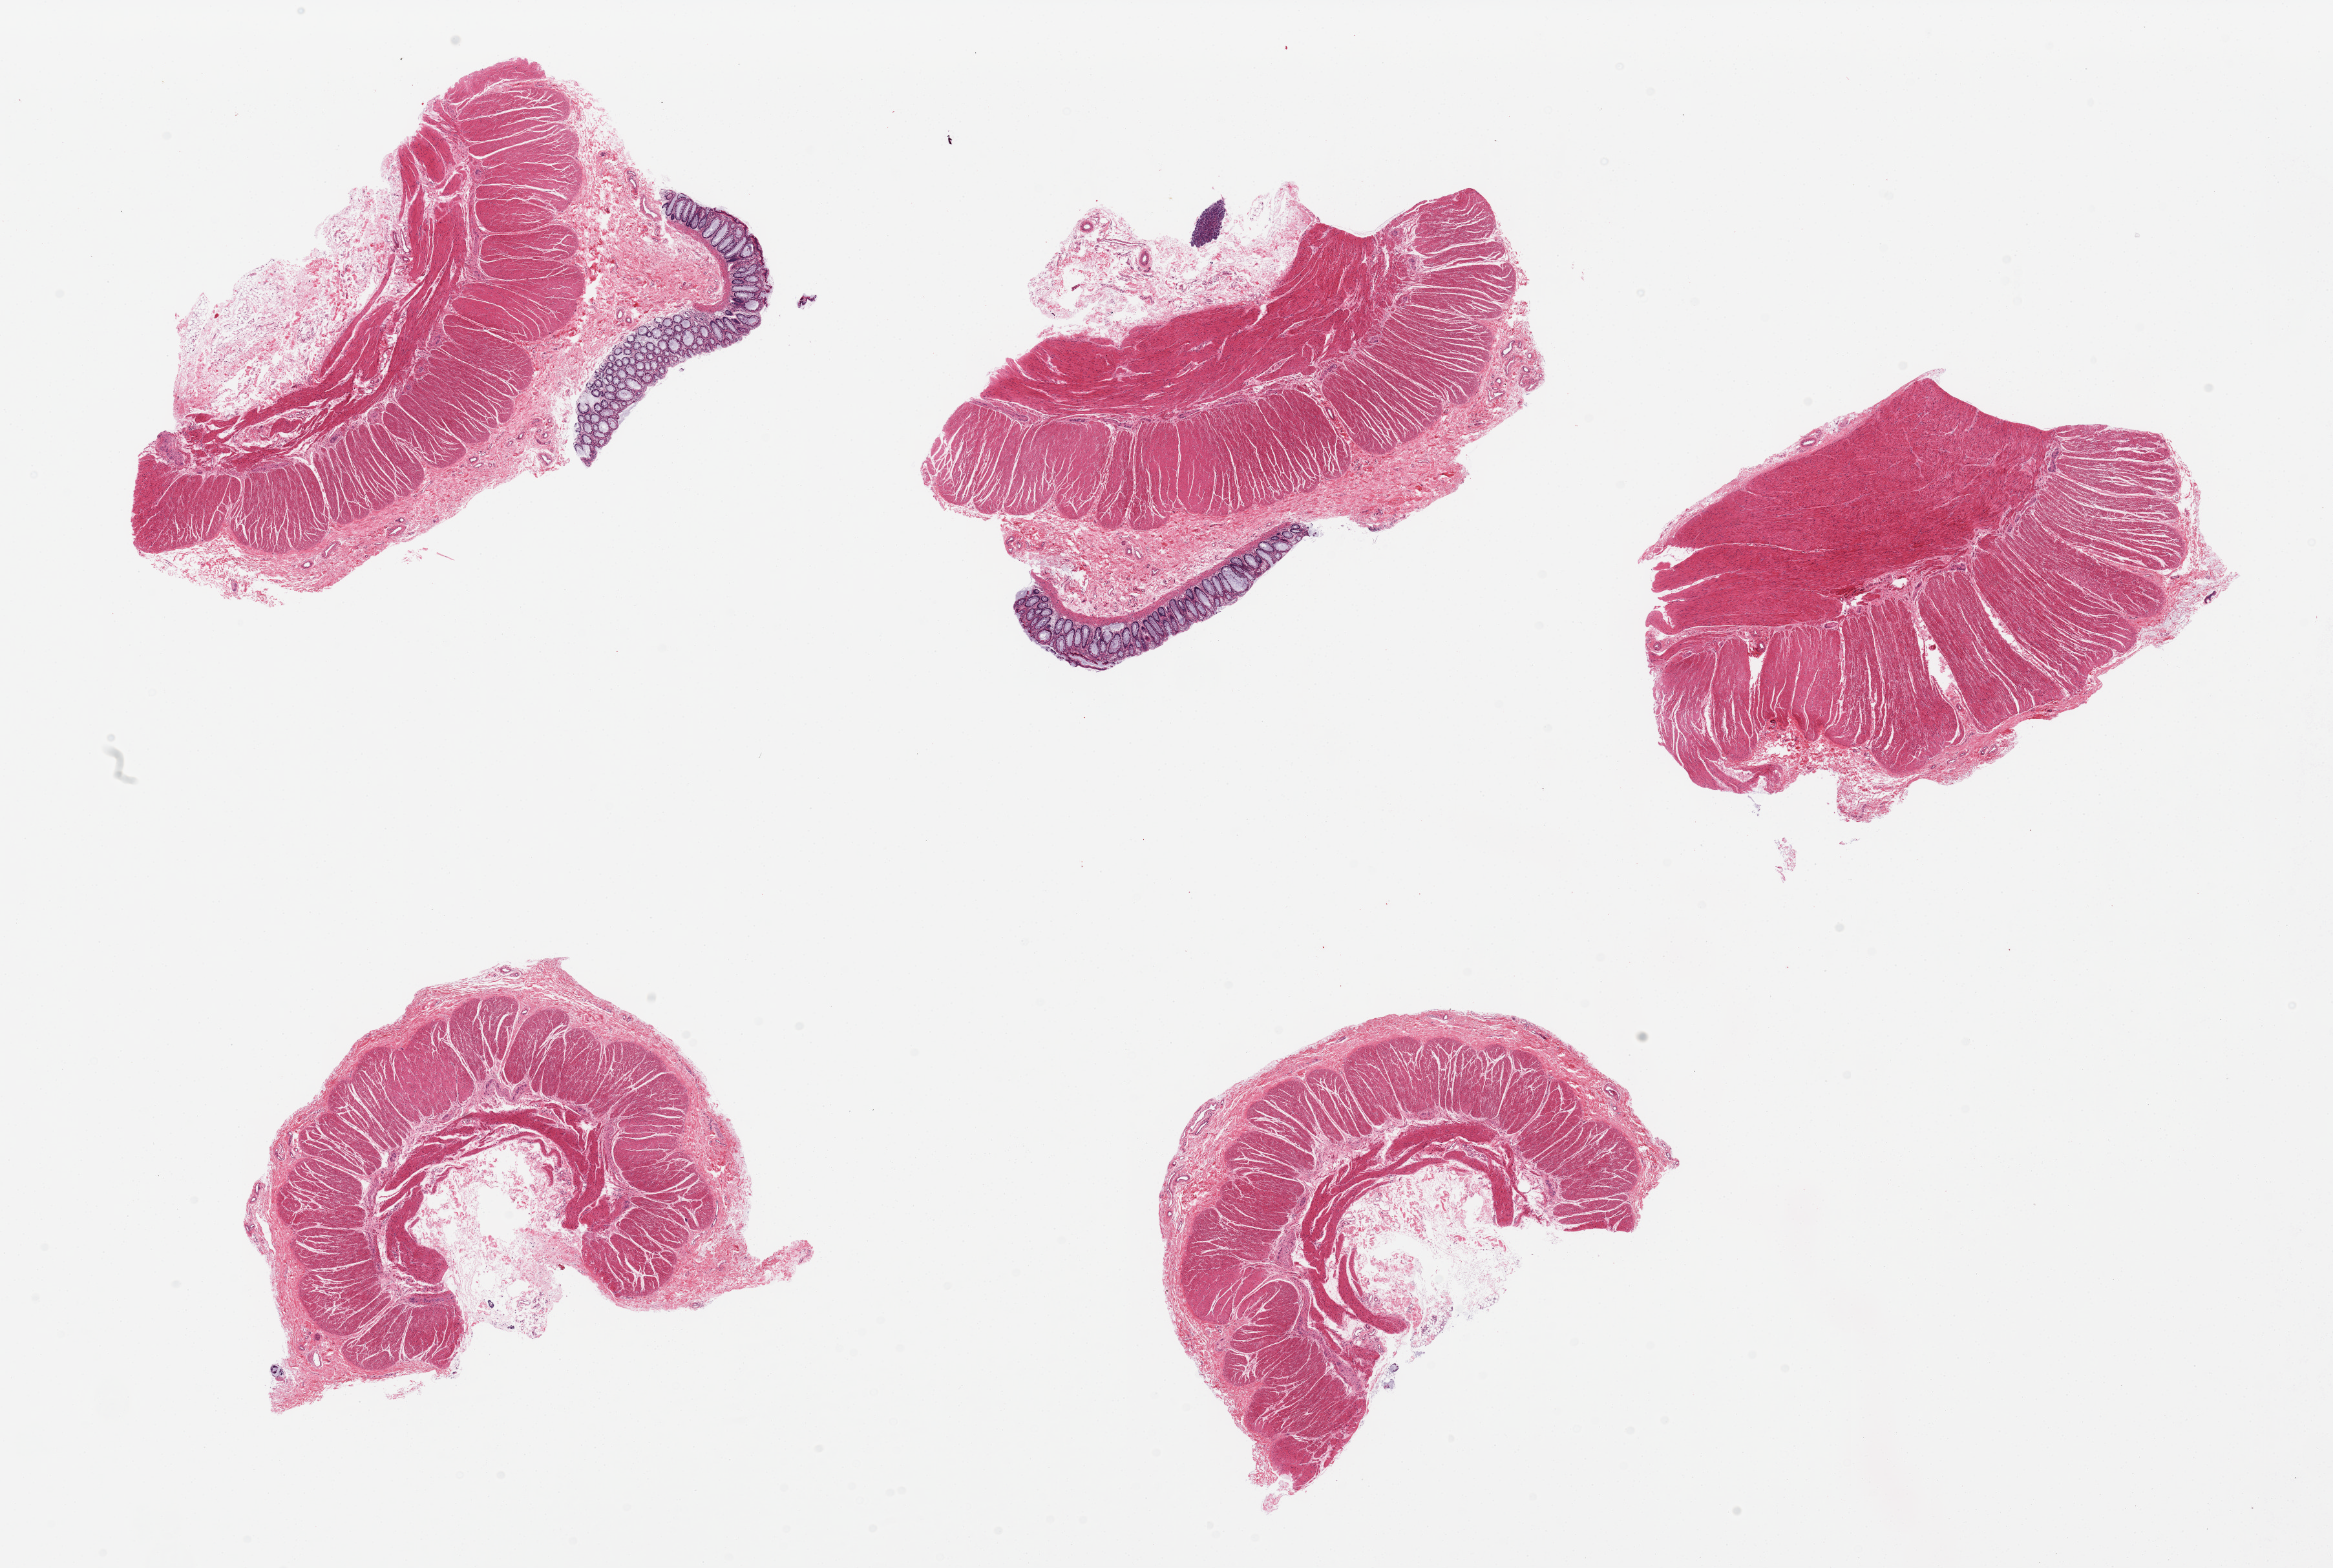
H&E whole-slide image, a low-resolution overview of the entire scanned area, about 28.5 x 19.2 mm (slide scanned at 20x); PAXgene-fixed, paraffin-embedded tissue; section of sigmoid colon (target tissue); tissue donor sample.
- review note (as recorded): 5 pieces: all have muscularis, 2 have mucosa [not target]